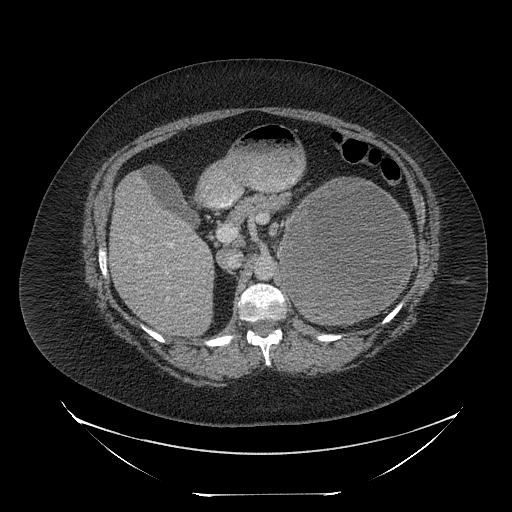
Contrast-enhanced abdominal CT, one axial slice. Position 143 of 205 along the scan axis. Reconstruction kernel STANDARD. Intravenous contrast given. Soft-tissue window (W 400 / L 40 HU). 2.5 mm slice thickness. 512 × 512 image matrix. Patient: female, 53 years. Case-level facts recorded for this patient, not image findings: diagnosis: adrenocortical carcinoma; tumour side: left adrenal.
Outlined on this slice (semi-automatic segmentation, software-assisted and operator-edited):
- mass: bounding box [x1, y1, x2, y2] px = [281, 179, 412, 320]